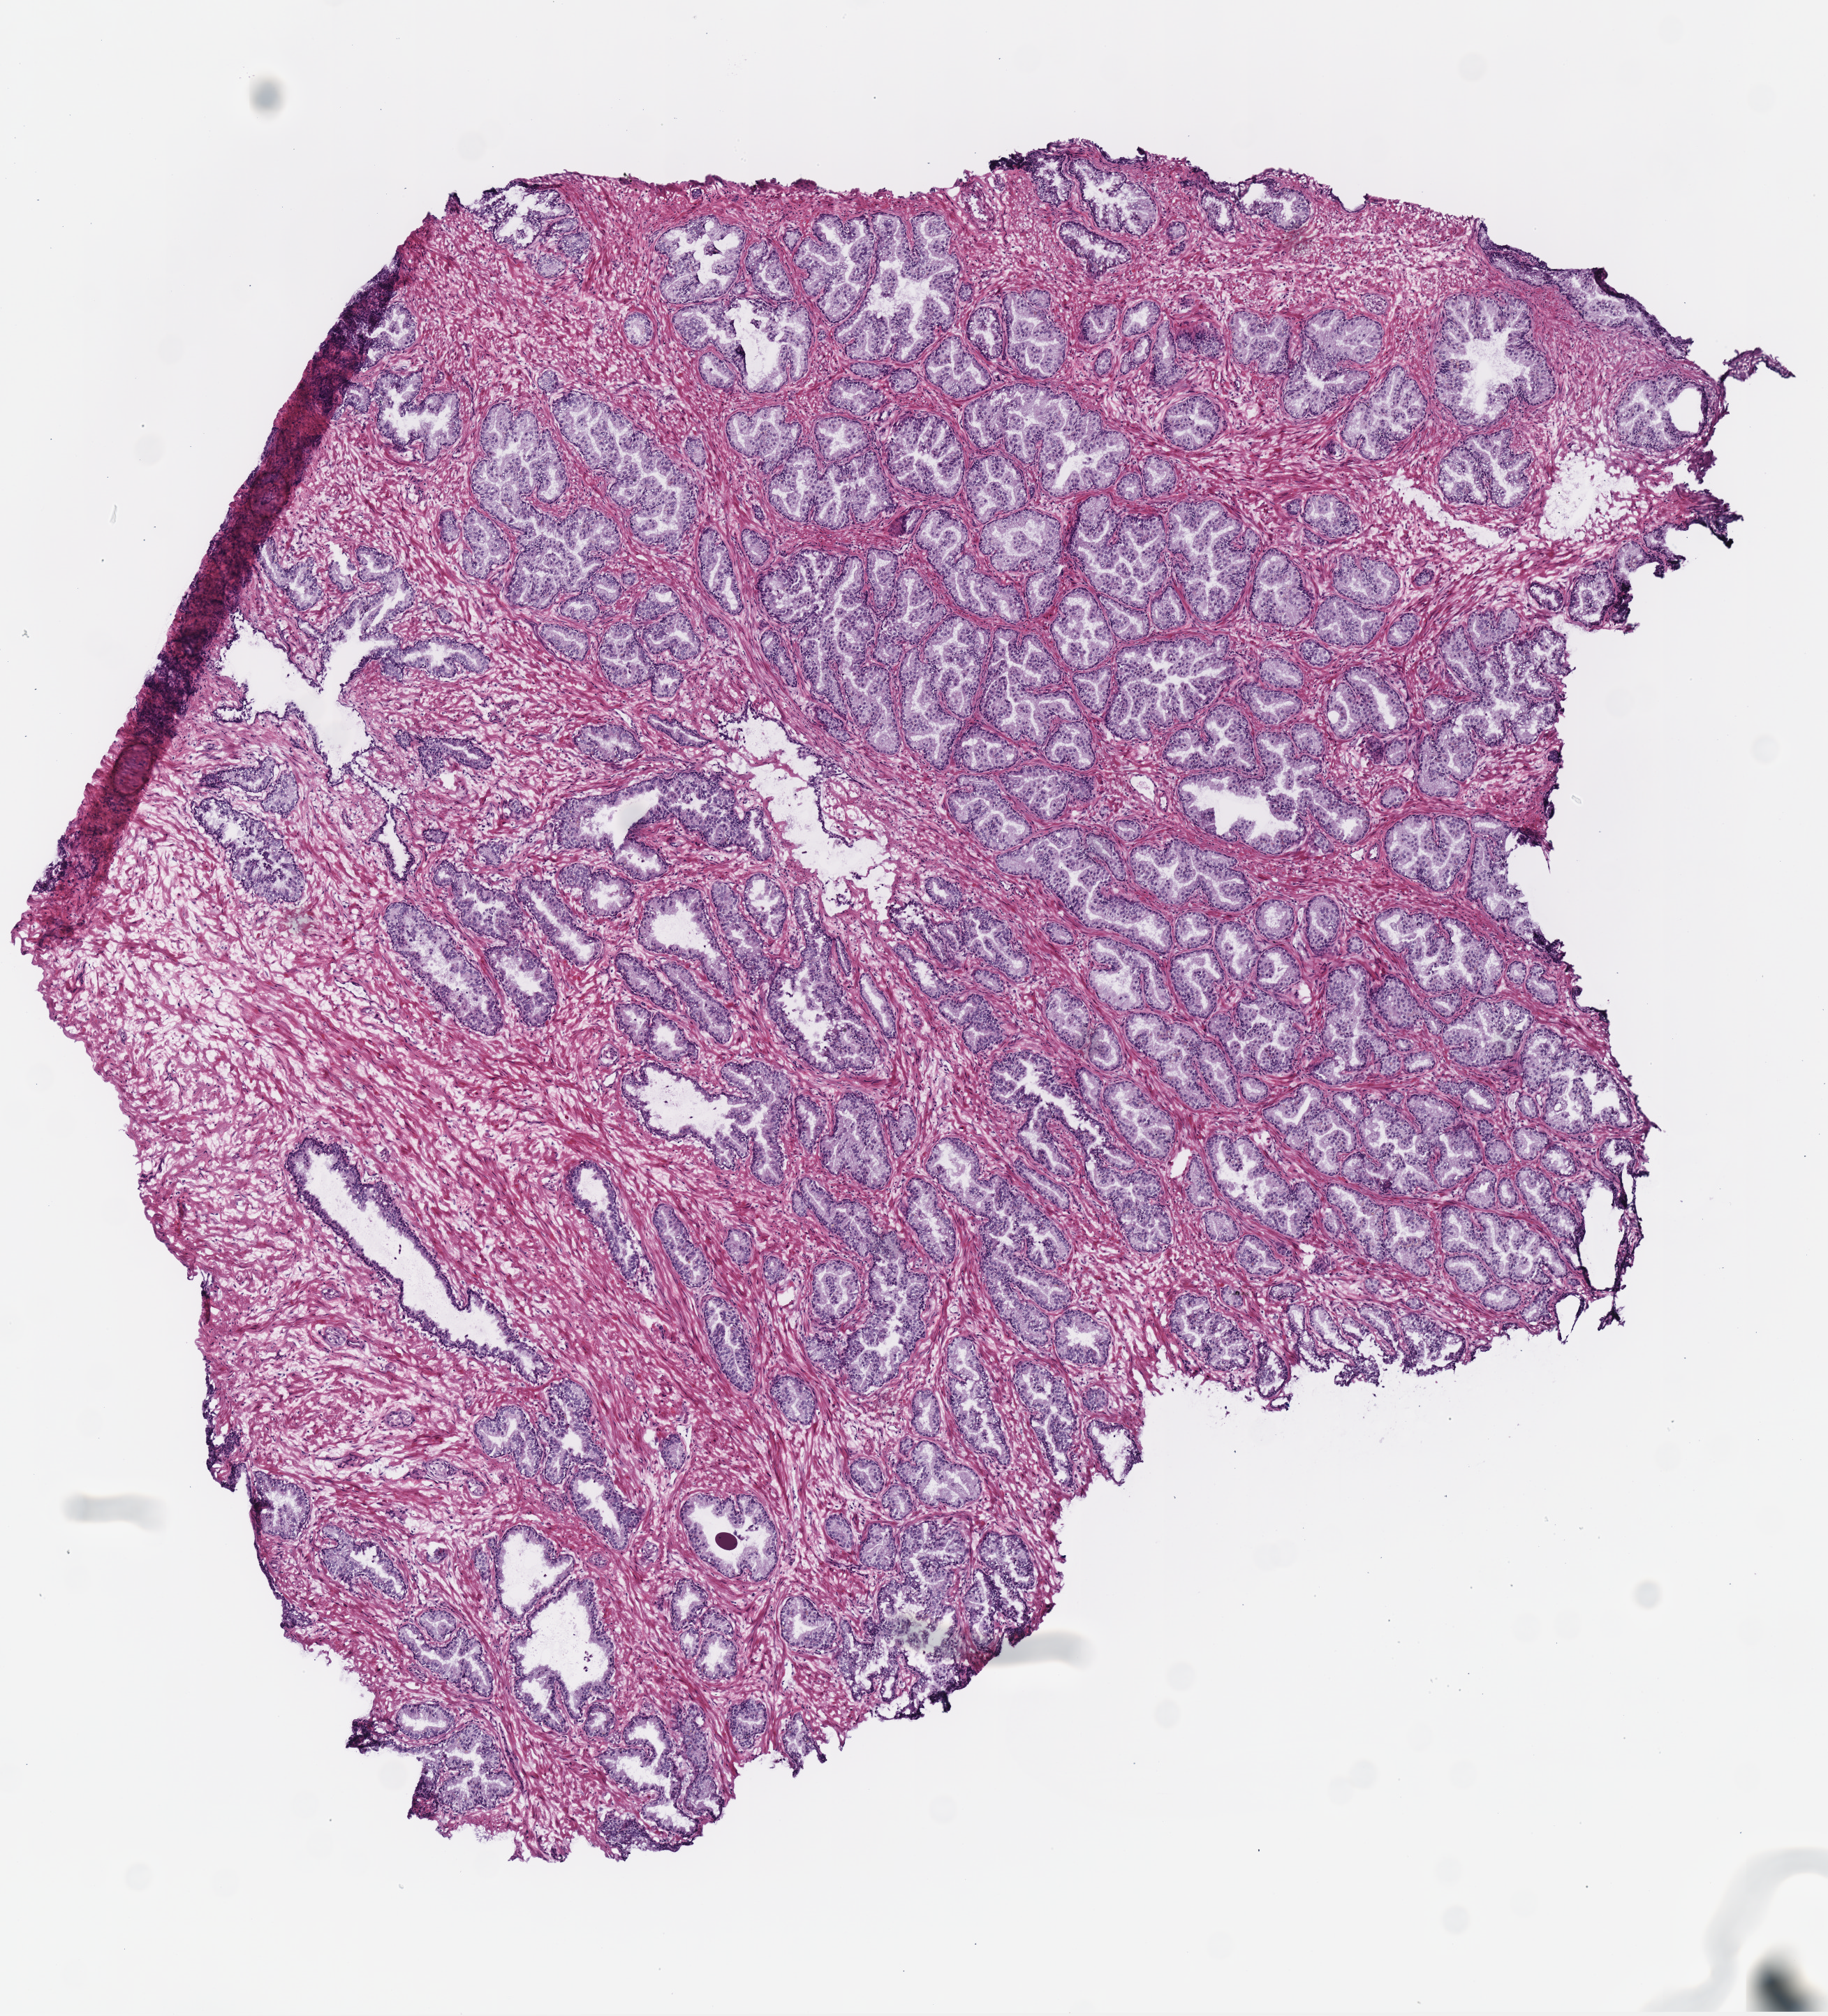
H&E whole-slide image — a low-resolution overview of the entire scanned area, about 5.2 x 5.7 mm, frozen section from the top of the tissue portion, prostate, solid tissue normal (non-tumour tissue) sample. Male patient; age at initial diagnosis 66 years.
This section: solid tissue normal sample (biorepository sample class). Patient diagnosis: Acinar cell carcinoma (prostate gland).